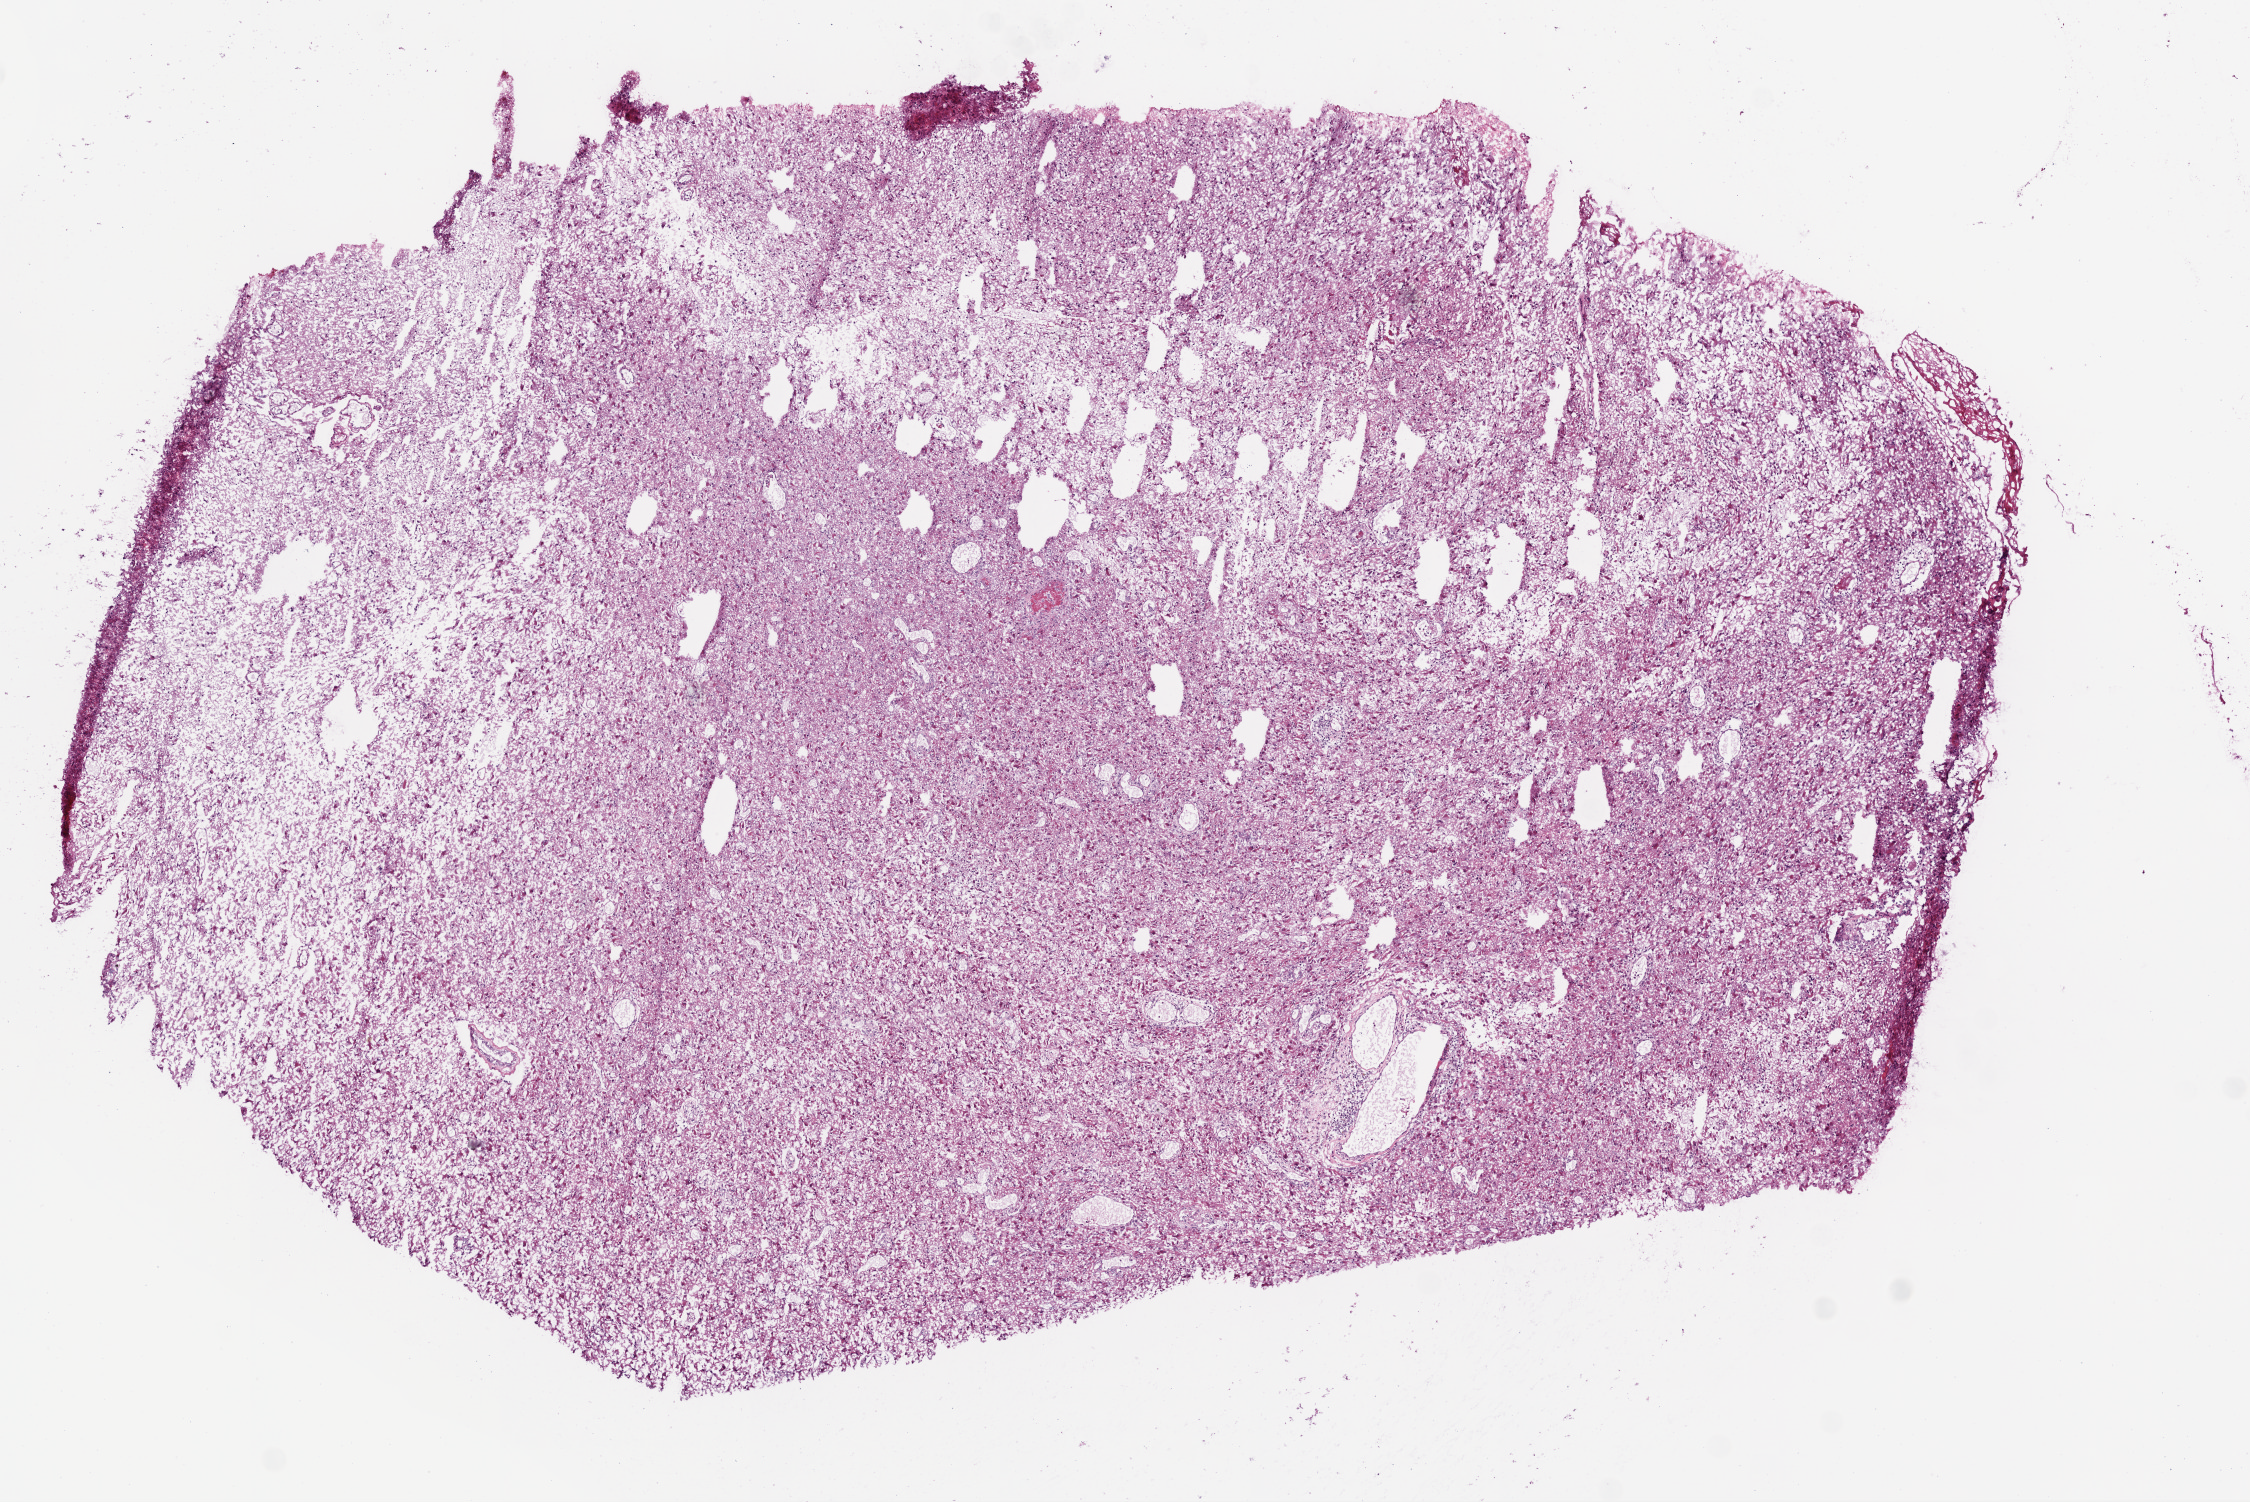
Hematoxylin and eosin (H&E) stained whole-slide image, shown as a low-resolution overview of the whole scanned area (about 9.0 x 6.0 mm, acquisition: 20x scan); frozen section from the bottom of the tissue portion; sample: primary tumour, brain. Male, age 56 years at initial diagnosis. Composition of this section per pathologist review: tumour cells 100%, tumour nuclei 80%, normal cells 0%, stromal cells 0%, necrosis 0%.
Histologic diagnosis: Glioblastoma.